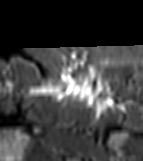
MRI of an extremity soft-tissue mass, one axial slice. Slice 52 of 81 in the series (ordered by position). STIR. MR volume resampled by the dataset authors to the PET/CT grid (not the native acquisition matrix). 143 × 161 image matrix, field of view 140 × 157 mm. Female patient. From the clinical record (not read from this slice): histological type: myxofibrosarcoma; grade: intermediate; site of the primary tumour: left thigh.
Outlined on this slice (expert contour drawn on MRI and transferred to this co-registered scan by the dataset authors):
- gross tumour volume including surrounding oedema: bounding box (x1, y1, x2, y2) in pixels: (28, 75, 116, 109)